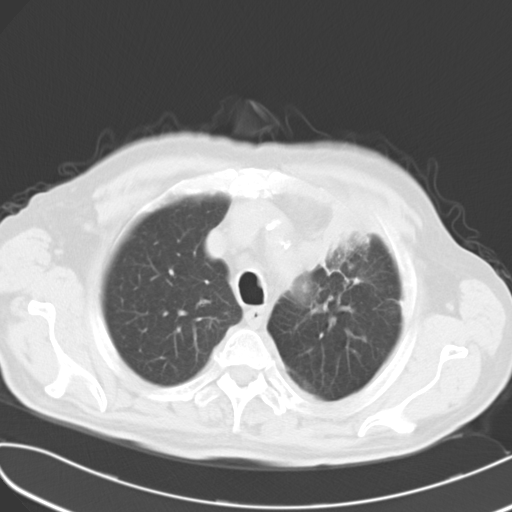
Chest CT, one axial slice; slice 22 of 27 in the series (ordered by position); 120 kVp; lung window (W 1500 / L -600 HU); 10 mm slice thickness; 512 × 512 image matrix, field of view 353 × 353 mm. Patient: male, 70 years. From the clinical record (not read from this slice): clinical TNM (as recorded): T2 N1 M3.
Structures marked on this image (bounding box drawn by a radiologist):
- lung tumour (recorded histology: small cell carcinoma): bounding box <294,200,363,280> (left, top, right, bottom; pixels)